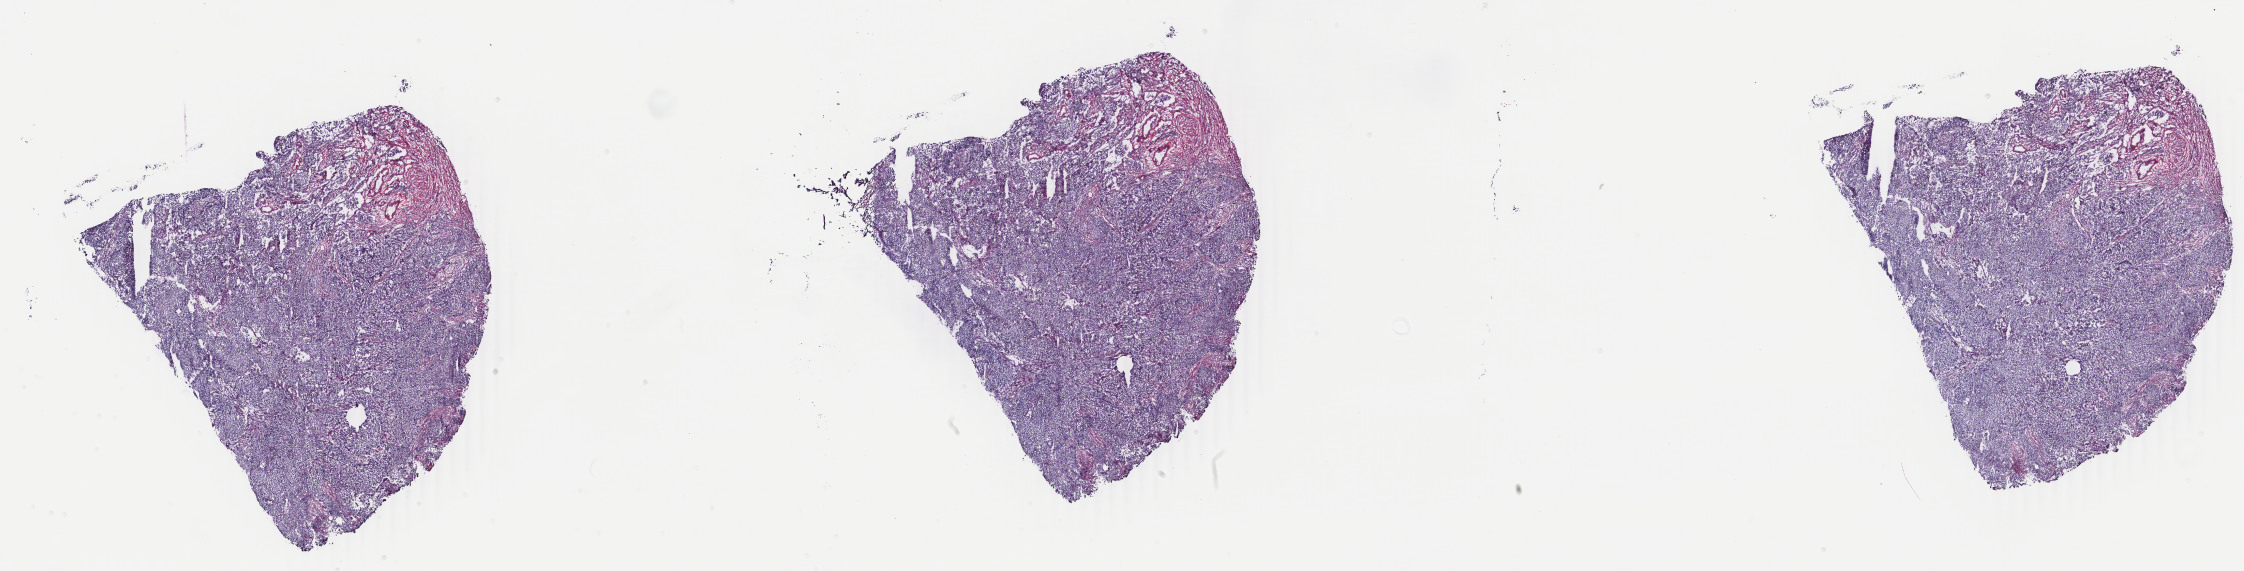
H&E whole-slide image — low-resolution overview of the scanned area, about 35.7 x 9.1 mm, frozen section, uterus, primary tumour sample. Patient: female, age at initial diagnosis 67 years. Histologic grade: G3 (poorly differentiated). Pathologist review of this section (percent, as recorded): tumour cells 90%, tumour nuclei 85%, normal cells 0%, stromal cells 10%, necrosis 0%. Inflammatory infiltration, as recorded: lymphocyte infiltration 0%, monocyte infiltration 0%, neutrophil infiltration 0%.
* FIGO stage: IIIC2
* diagnosis: Endometrioid adenocarcinoma, NOS (endometrium)